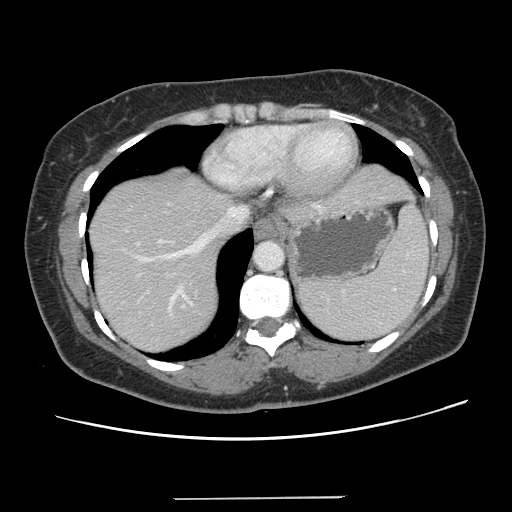
Contrast-enhanced abdominal CT, one axial slice. Slice 114 of 141 in the series (ordered by position). Intravenous contrast given. Soft-tissue window (W 400 / L 40 HU). 2.5 mm slice thickness. 512 × 512 image matrix, field of view 366 × 366 mm. Female patient, age 53 years. Case-level facts recorded for this patient, not image findings: diagnosis: colorectal cancer liver metastases, imaged before liver resection; multiple liver metastases: no; largest metastasis: 14.5 cm; chemotherapy before resection: yes.
Annotated regions visible in this slice (manually delineated by an expert):
- hepatic veins: bounding box [x1, y1, x2, y2] px = [114, 205, 316, 298]
- liver: [89, 165, 410, 353]
- planned liver remnant (the part of the liver to remain after resection): [89, 210, 232, 353]
- portal vein (with intrahepatic branches): [136, 239, 193, 316]